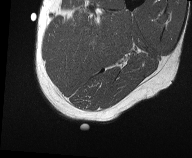
MRI of an extremity soft-tissue mass, one axial slice; position 7 of 61 along the scan axis; MR volume resampled by the dataset authors to the PET/CT grid (not the native acquisition matrix); 3.27 mm slice thickness; 192 × 158 image matrix, field of view 187 × 154 mm. Male patient. Case-level facts recorded for this patient, not image findings: histological type: pleiomorphic liposarcoma; grade: high; site of the primary tumour: left thigh.
Annotated regions visible in this slice (expert contour drawn on MRI and transferred to this co-registered scan by the dataset authors):
- gross tumour volume including surrounding oedema: bounding box (x1, y1, x2, y2) in pixels: (73, 12, 112, 38)